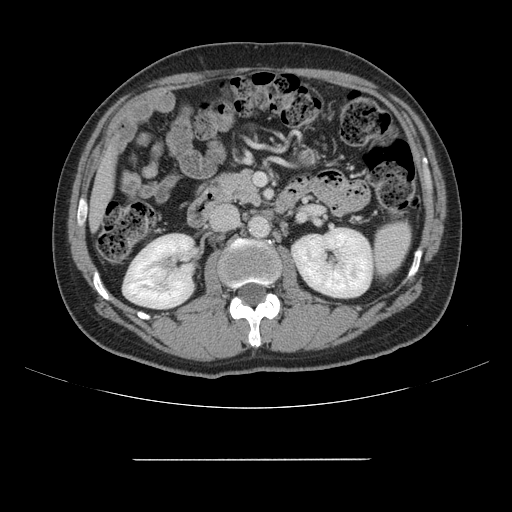
Contrast-enhanced abdominal CT, one axial slice. Position 57 of 164 along the scan axis. 120 kVp. Intravenous contrast given. Soft-tissue window (W 400 / L 40 HU). 512 × 512 image matrix. Male patient, age 54 years. From the clinical record (not read from this slice): diagnosis: colorectal cancer liver metastases, imaged before liver resection; multiple liver metastases: yes; largest metastasis: 1 cm.
Outlined on this slice (manually delineated by an expert):
- liver: box from (x=92, y=158) to (x=113, y=223) px
- planned liver remnant (the part of the liver to remain after resection): (x=92, y=157)–(x=113, y=224)